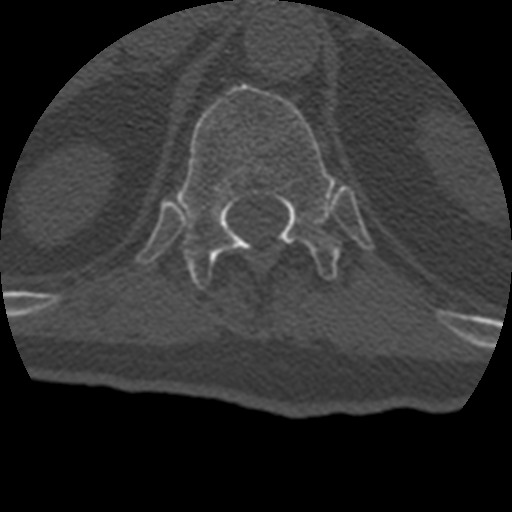
CT including the spine, one axial slice; reconstruction kernel STANDARD; 120 kVp; bone window (W 1800 / L 400 HU); 512 × 512 image matrix, field of view 160 × 160 mm. Patient age 69 years. Case-level facts recorded for this patient, not image findings: primary cancer: prostate.
Structures marked on this image (semi-automatic segmentation, software-assisted and operator-edited):
- T12 vertebra: box from (x=177, y=84) to (x=341, y=288) px